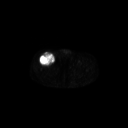
FDG PET of an extremity soft-tissue mass (from a PET/CT study), one axial slice. Position 294 of 311 along the scan axis. 3.27 mm slice thickness. 128 × 128 image matrix. Patient: male, 56 years. From the clinical record (not read from this slice): histological type: pleiomorphic leiomyosarcoma; grade: intermediate; site of the primary tumour: right thigh.
Outlined on this slice (expert contour drawn on MRI and transferred to this co-registered scan by the dataset authors):
- gross tumour volume including surrounding oedema: bounding box (x1, y1, x2, y2) in pixels: (39, 52, 55, 66)
- gross tumour volume (mass): (39, 52, 55, 66)